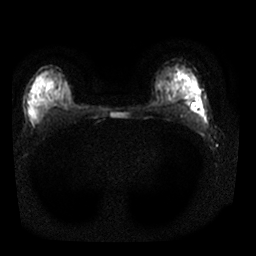
Breast MRI, one axial slice; position 14 of 25 along the scan axis; diffusion-weighted series; image 2 of 4 stored at this slice position (different b-values; order by instance number); 1.5 T; 4 mm slice thickness; 256 × 256 image matrix, field of view 320 × 320 mm. Female patient.
Structures marked on this image (outlined manually by an expert reader):
- tumour on diffusion-weighted imaging: box from (x=191, y=108) to (x=197, y=112) px